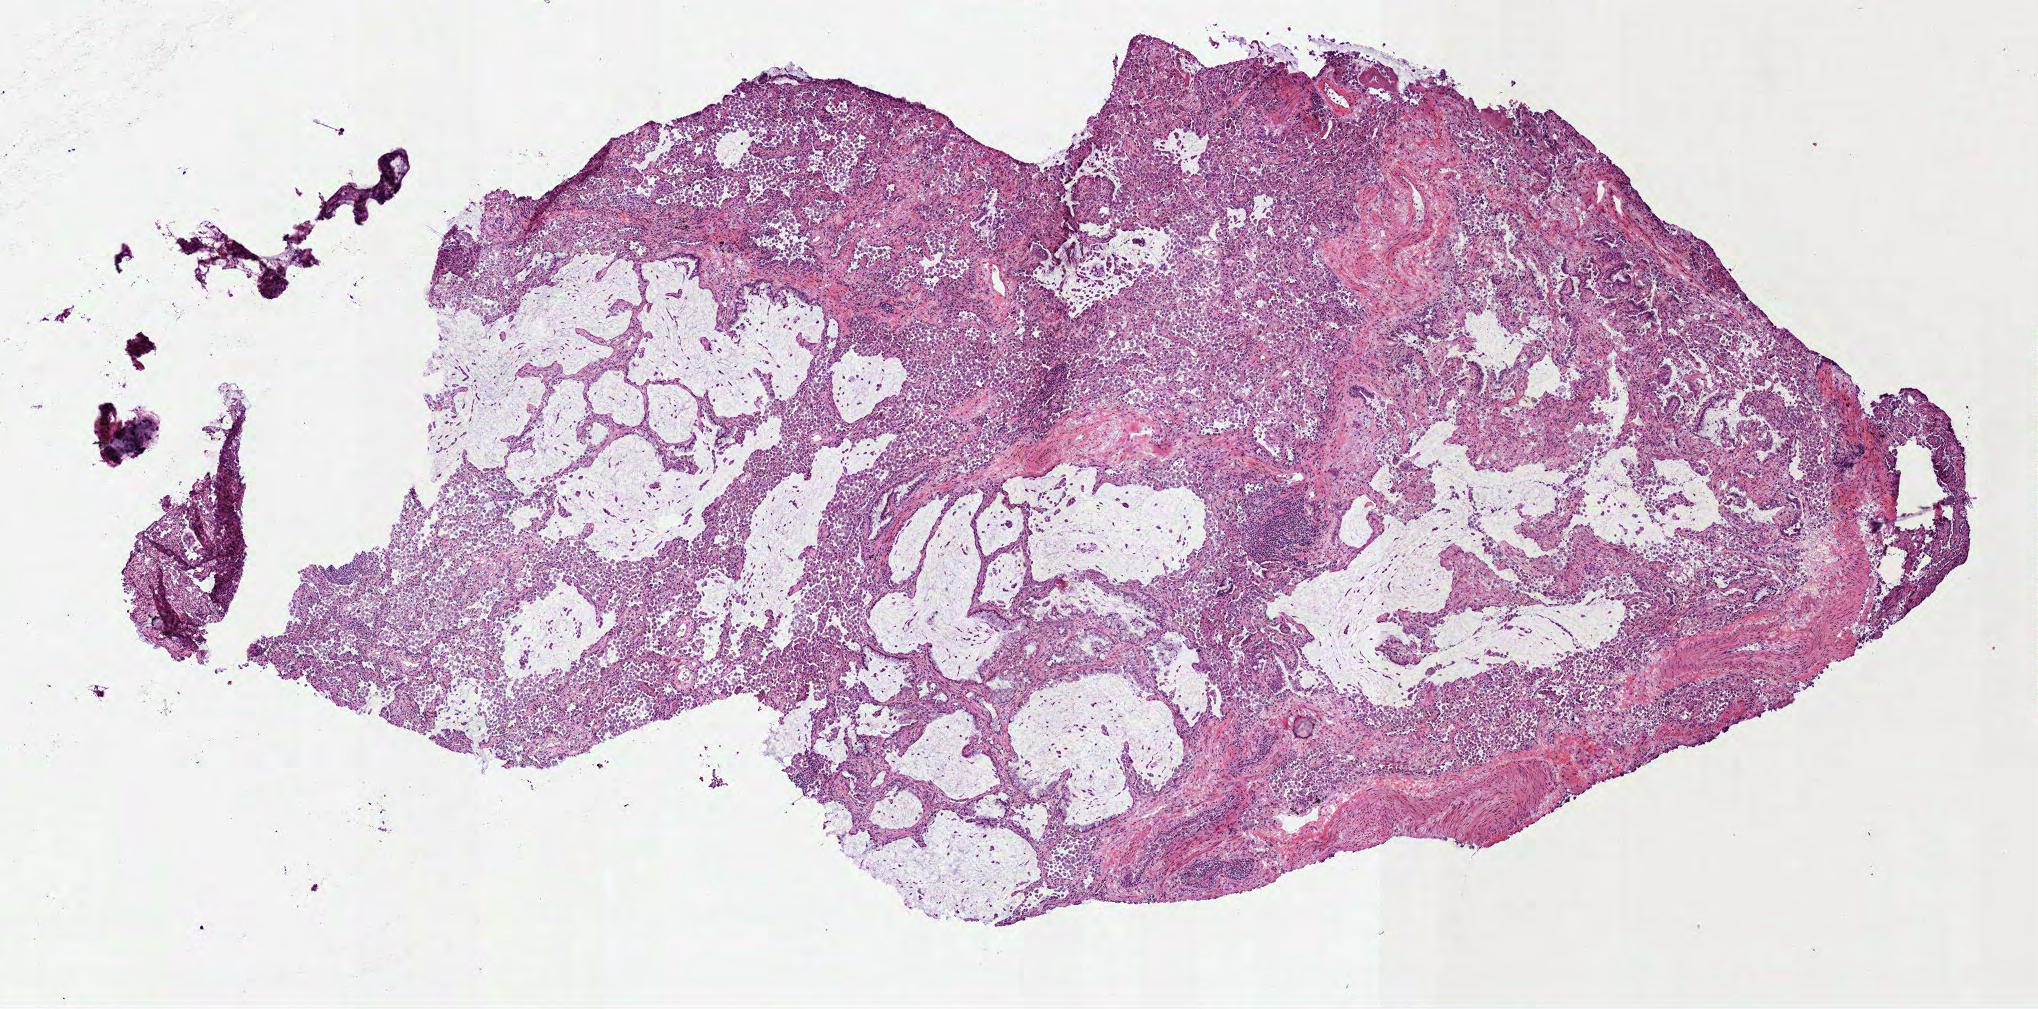
H&E-stained whole-slide image — low-resolution overview of the scanned area, about 8.2 x 4.1 mm; frozen section from the bottom of the tissue portion; sample: primary tumour, lung. Patient: female, age at initial diagnosis 75 years. Slide review estimates, as recorded: tumour cells 80%, tumour nuclei 70%, normal cells 0%, stromal cells 20%, necrosis 0%.
• diagnosis: Adenocarcinoma, NOS (upper lobe, lung)
• AJCC pathologic stage: IA